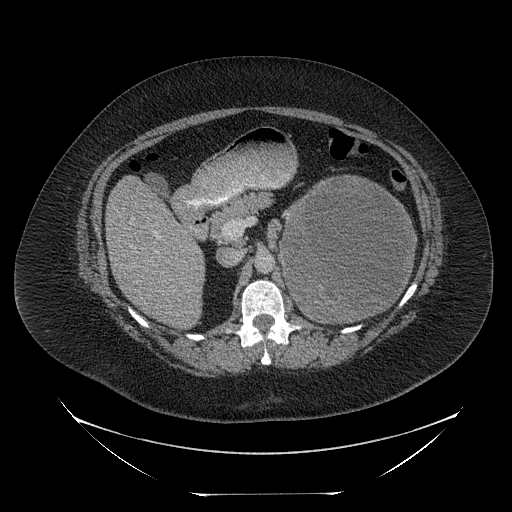
Contrast-enhanced abdominal CT, one axial slice. Position 138 of 205 along the scan axis. Reconstruction kernel STANDARD. Intravenous contrast given. Soft-tissue window (W 400 / L 40 HU). 2.5 mm slice thickness. 512 × 512 image matrix, field of view 500 × 500 mm. Female patient, age 53 years. Case-level facts recorded for this patient, not image findings: diagnosis: adrenocortical carcinoma; tumour side: left adrenal; tumour size at pathology: 17 cm; Ki-67 index: 20 %; stage (as recorded): 3.
Annotated regions visible in this slice (semi-automatically segmented with operator editing):
- mass: bounding box [x1, y1, x2, y2] px = [282, 178, 412, 321]